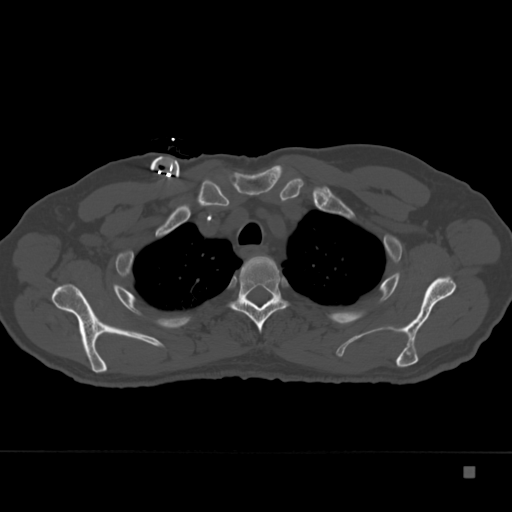
CT including the spine, one axial slice. Position 287 of 332 along the scan axis. Bone window (W 1800 / L 400 HU). 1.5 mm slice thickness. 512 × 512 image matrix. Patient: male, 72 years. From the clinical record (not read from this slice): primary cancer: skeletal.
Outlined on this slice (semi-automatically segmented with operator editing):
- T3 vertebra: bounding box [x1, y1, x2, y2] px = [230, 256, 288, 333]